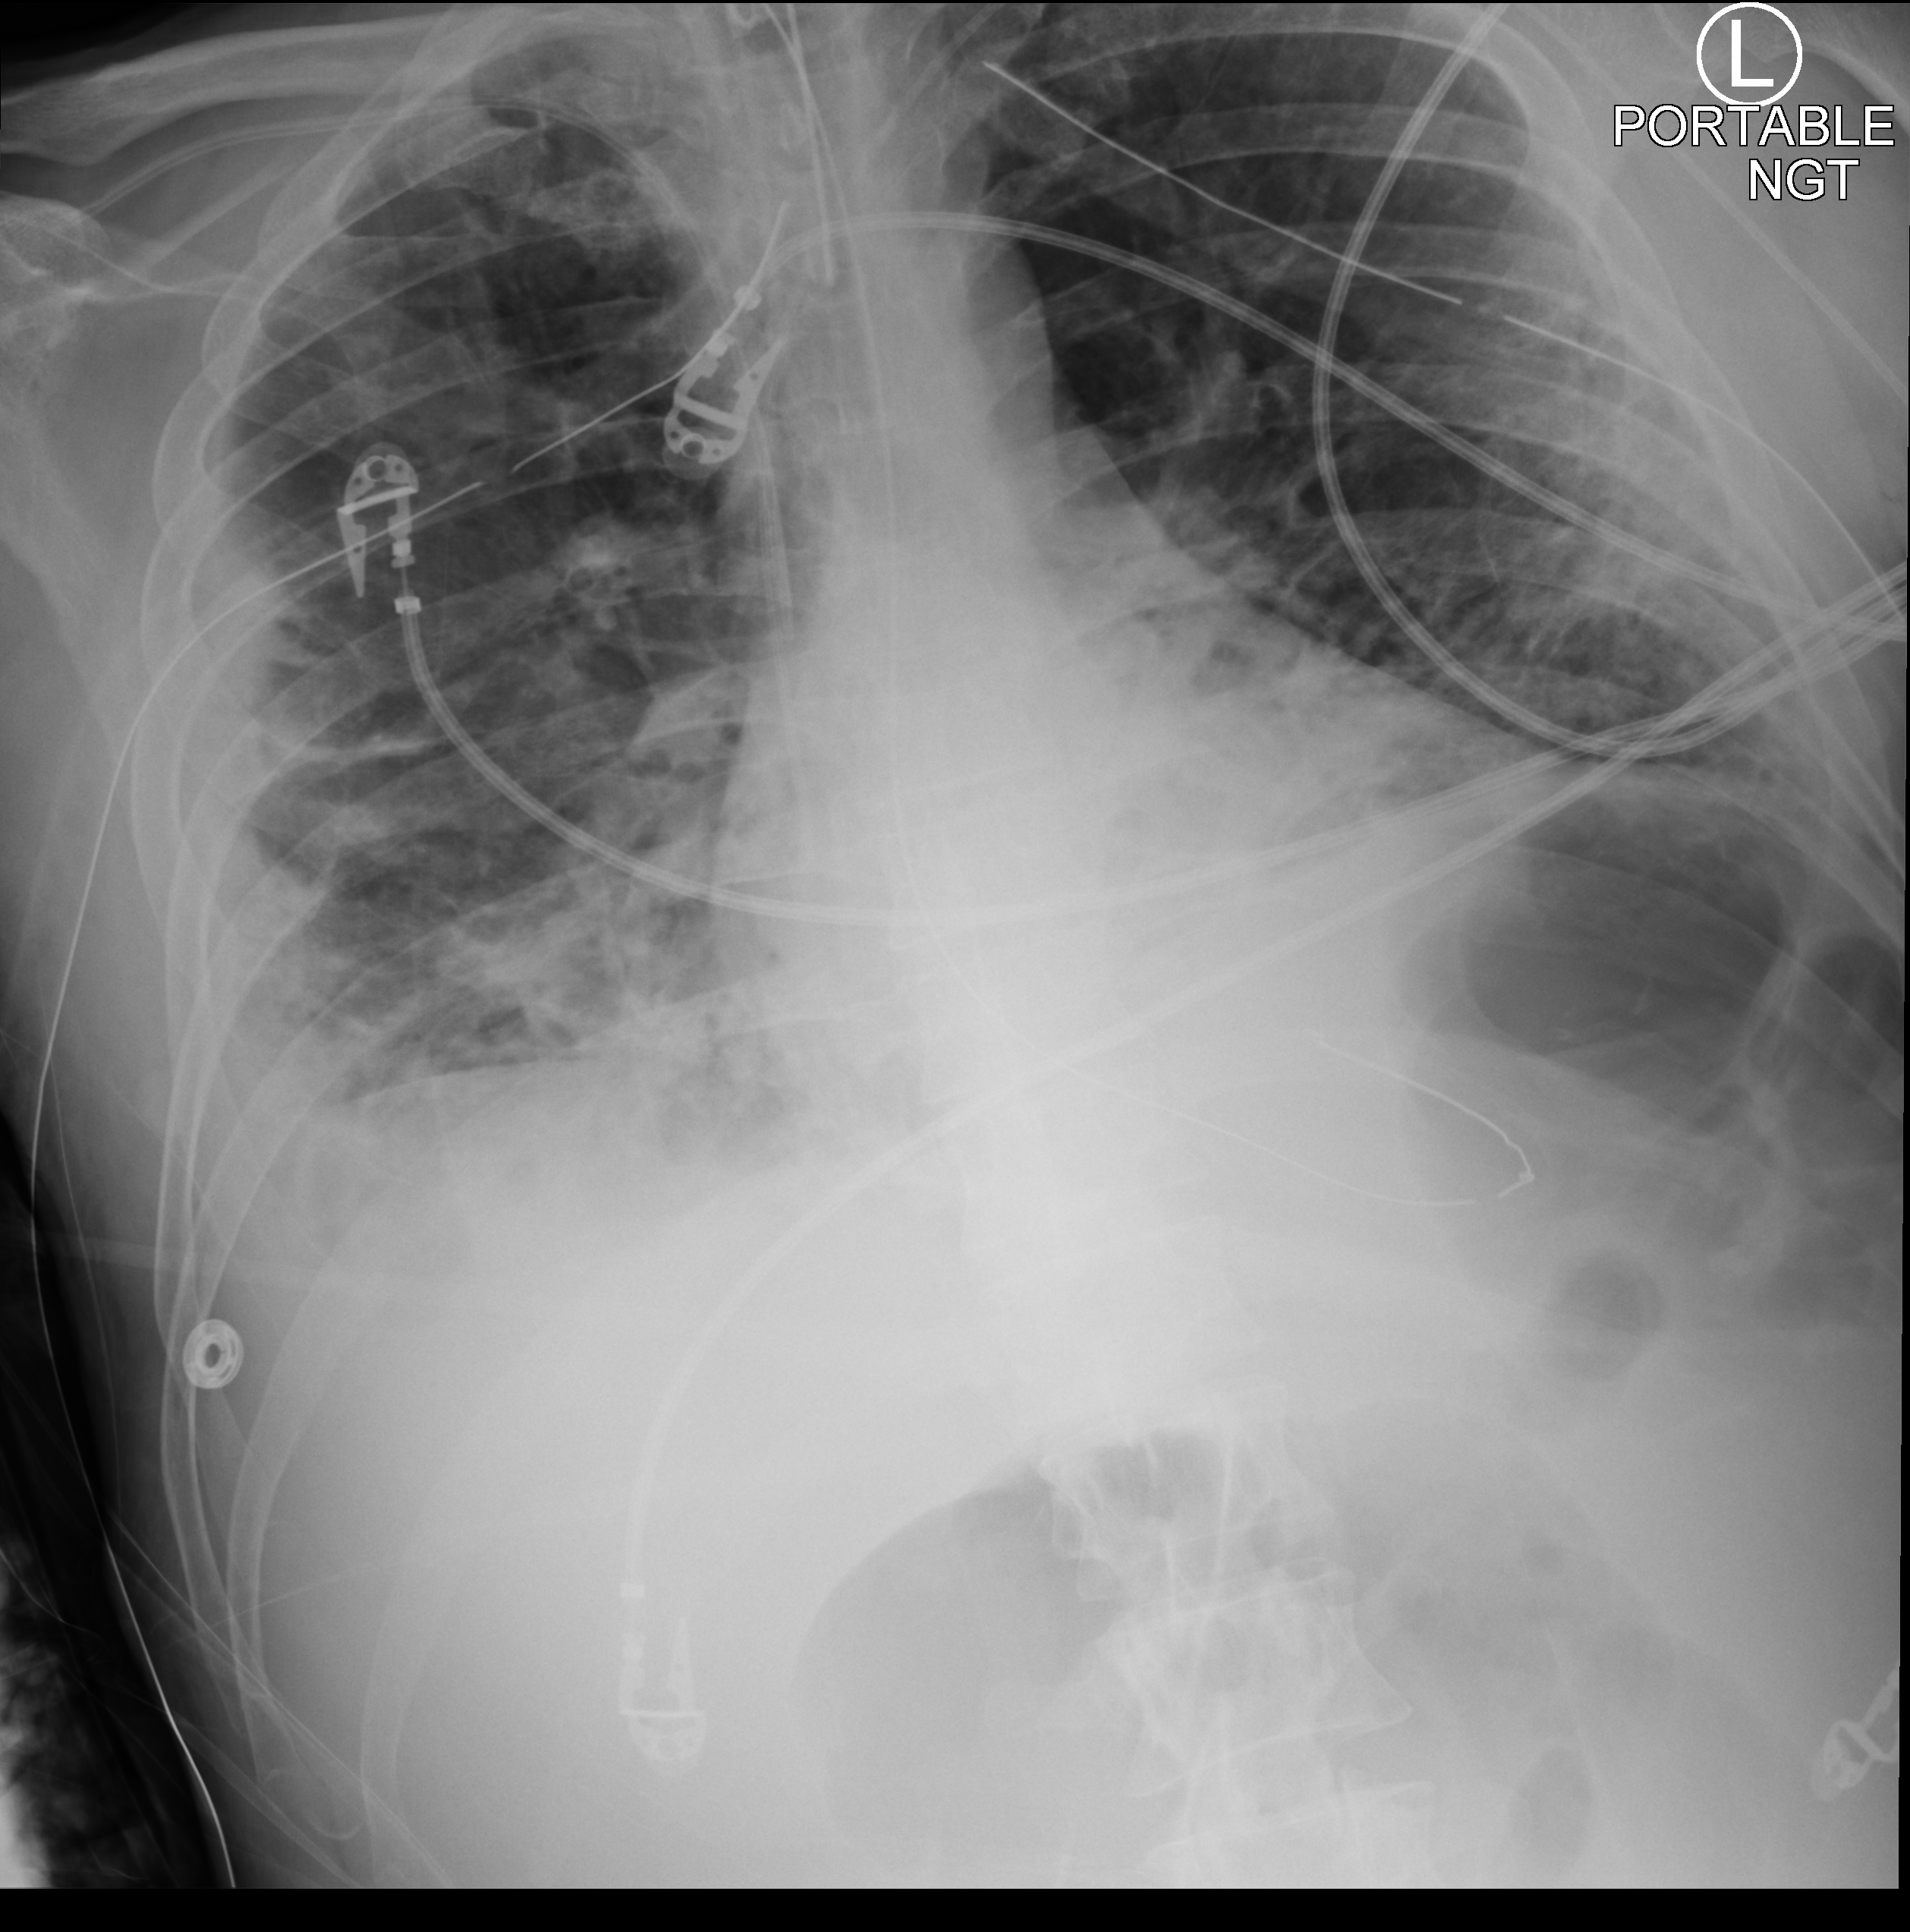
Portable chest radiograph. Male patient hospitalised with COVID-19, age 18–59 years.
Admission-level facts for this patient (not findings on this image; timing relative to this image not recorded): admitted to intensive care during this hospital stay: yes; COPD (admission record): no; diabetes (admission record): yes.